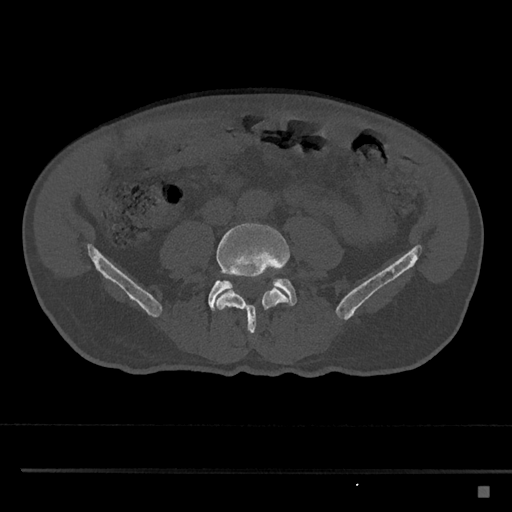
CT including the spine, one axial slice; slice 615 of 797 in the series (ordered by position); 120 kVp; bone window (W 1800 / L 400 HU); 0.5 mm slice thickness; 512 × 512 image matrix, field of view 391 × 391 mm. Male patient, age 59 years. From the clinical record (not read from this slice): primary cancer: prostate.
Outlined on this slice (semi-automatic segmentation, software-assisted and operator-edited):
- L4 vertebra: bounding box [x1, y1, x2, y2] px = [216, 223, 290, 334]
- L5 vertebra: [208, 278, 297, 311]